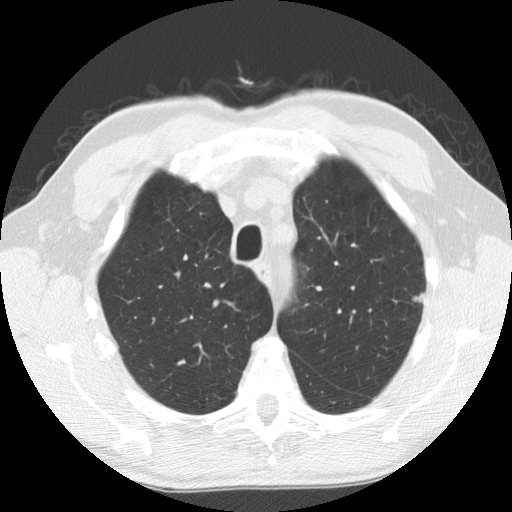
Low-dose screening chest CT, axial slice. Third screening round (two years after baseline). Lung window (W 1500 / L -600 HU). 2.5 mm slice thickness. Male participant, aged 63 years at enrolment. Current smoker at enrolment.
Expert reader's lesion annotation, bounding box <398,276,437,311> (left, top, right, bottom; pixels). Reader record for this screening exam (exam-level; its link to the box is not recorded): non-calcified nodule or mass ≥4 mm, left upper lobe, 8 × 6 mm, smooth margins, ground glass attenuation, pre-existing on the prior screen: yes; interval growth: yes. Later outcome: lung cancer diagnosed 52 days after this screen — adenocarcinoma, NOS, left upper lobe, well differentiated (G1), stage IB (AJCC 6th edition), 5 mm at pathology.